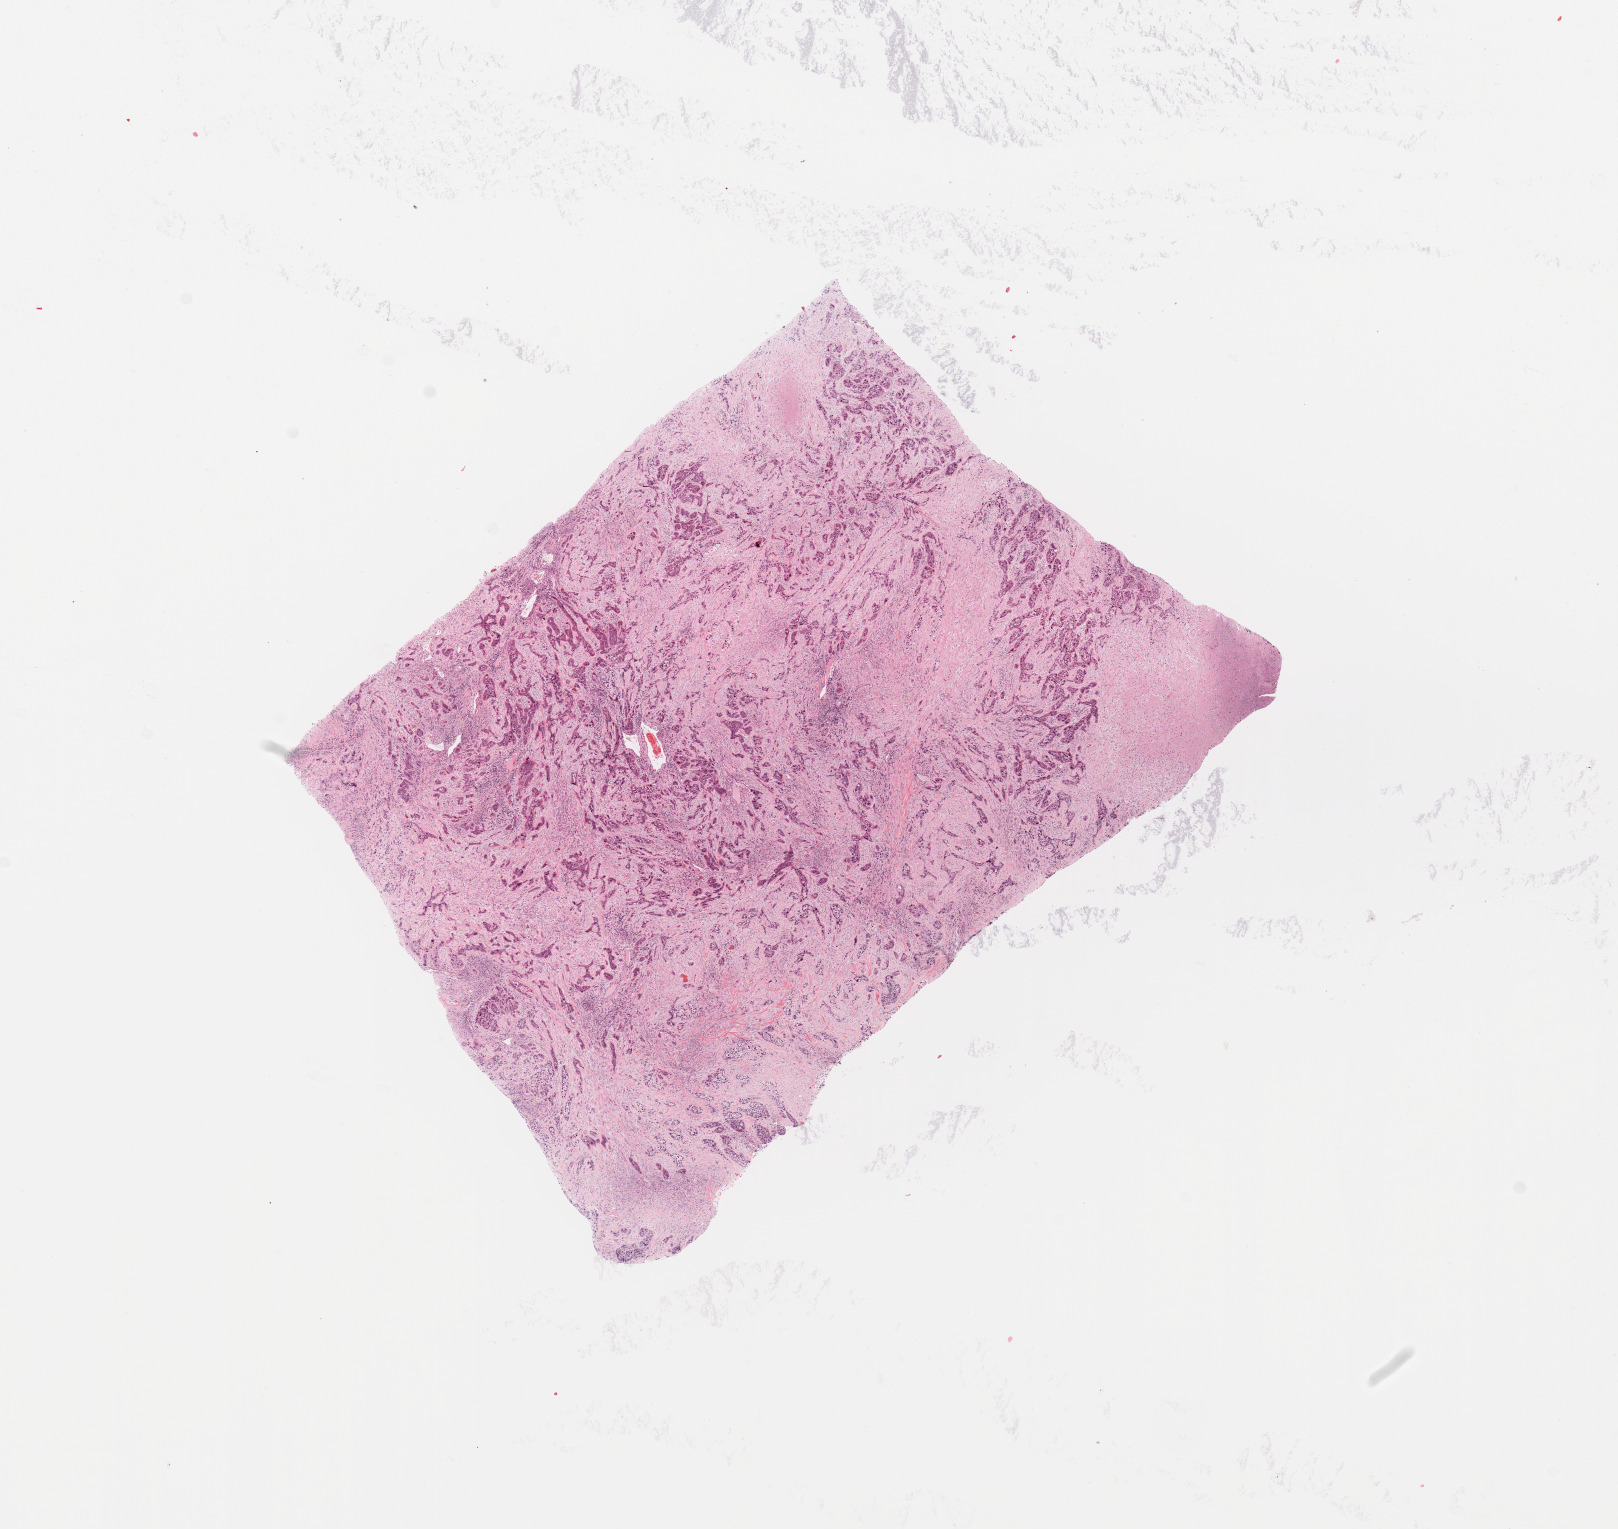
Whole-slide histology image, Hematoxylin and eosin (H&E) stained, whole scanned area (about 12.8 x 12.1 mm, slide scanned at 20x) shown as a low-resolution overview, tumour tissue sample, sampled site: lung. 66-year-old male patient. Histologic grade: G3 (poorly differentiated). Slide review estimates, as recorded: tumour nuclei 50%, necrosis 5%.
Diagnosis: Adenocarcinoma, NOS. Primary tumour site (as recorded): right upper lobe. AJCC pathologic stage: IIA.